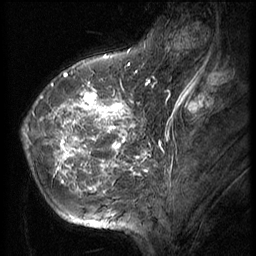
Breast MRI (dynamic contrast-enhanced), one sagittal slice; slice 18 of 56 in the series (ordered by position); 3 images stored at this slice position (order not interpretable as contrast timing); 1.5 T; TE 4.2 ms, TR 9 ms; 2.5 mm slice thickness; 256 × 256 image matrix, field of view 180 × 180 mm. Female patient, age 49 years. From the clinical record (not read from this slice): setting: breast cancer imaged before/during neoadjuvant chemotherapy; receptor status: HER2-positive.
Outlined on this slice (semi-automatically segmented with operator editing):
- analysis volume of interest (the breast-tissue region the enhancement analysis was run in; not a lesion): bounding box (x1, y1, x2, y2) in pixels: (21, 79, 139, 203)
- tumour enhancement mask (voxels above the 140 % enhancement threshold inside the analysis volume of interest): (24, 82, 138, 192)